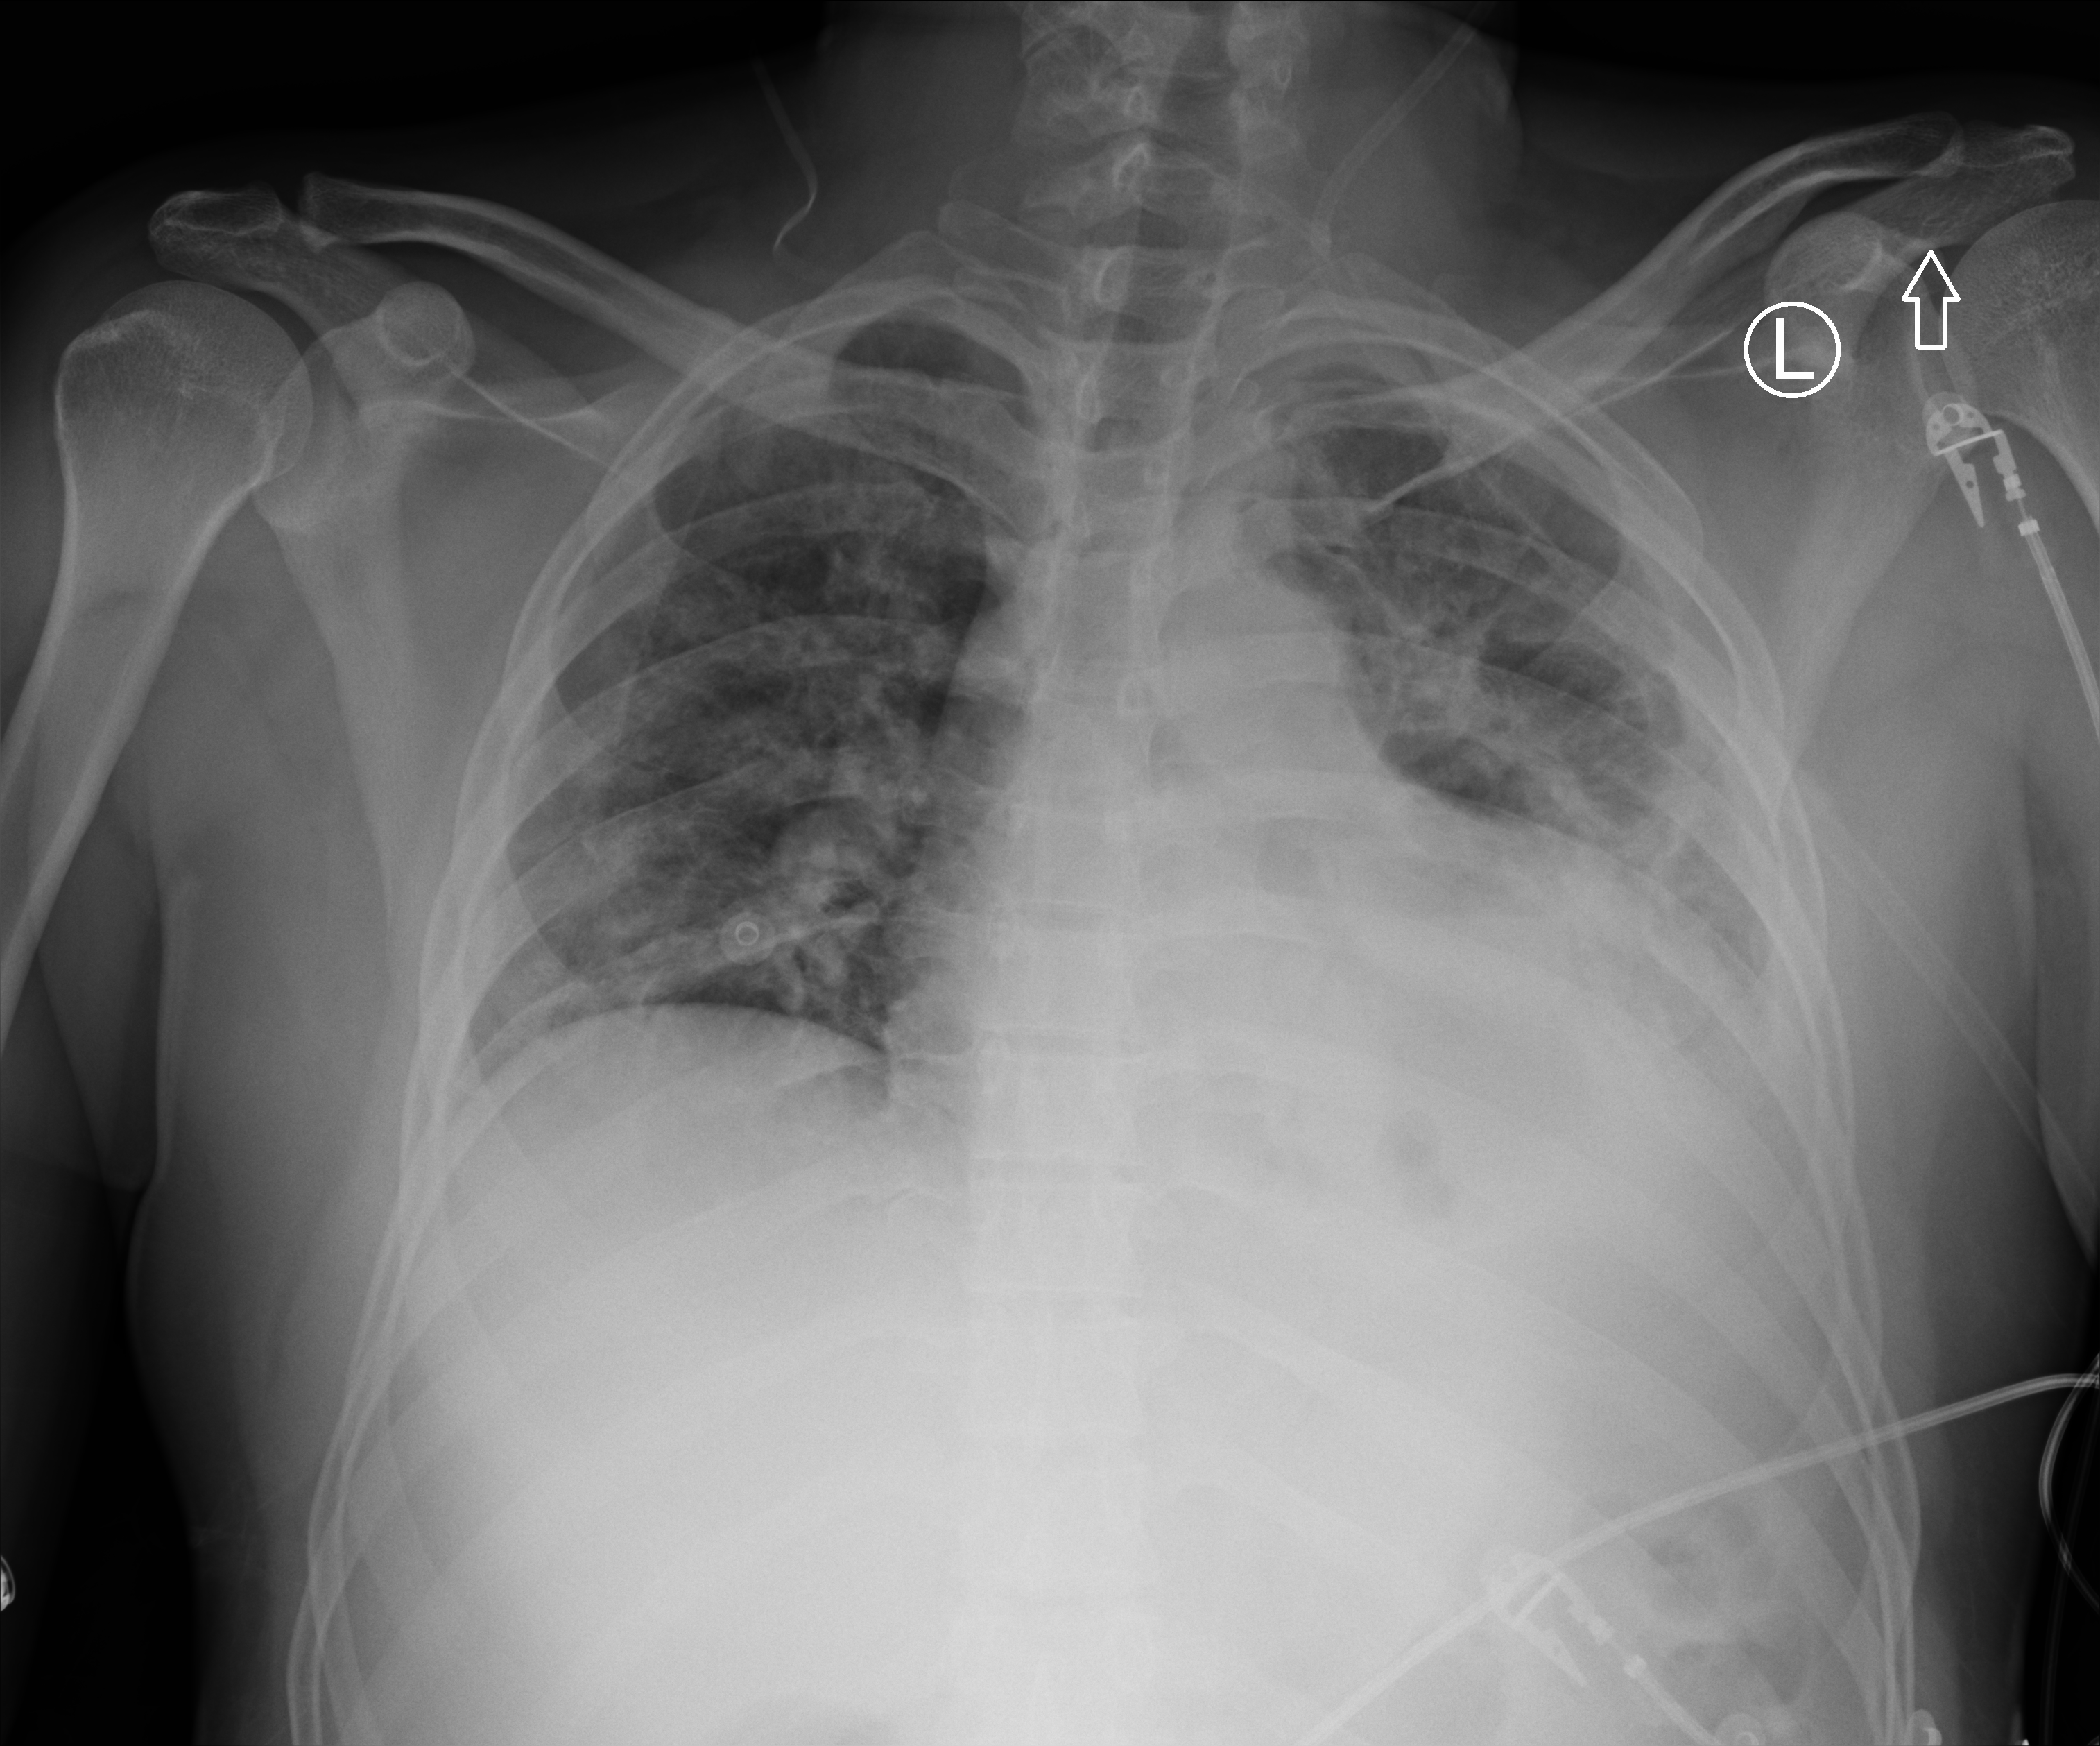
Bedside chest radiograph (computed radiography). Patient hospitalised with COVID-19; male, aged 18–59 years.
Hospital-stay facts (about this admission, not read from this image; timing relative to this image not recorded): mechanically ventilated during this hospital stay: yes; admitted to intensive care during this hospital stay: yes.